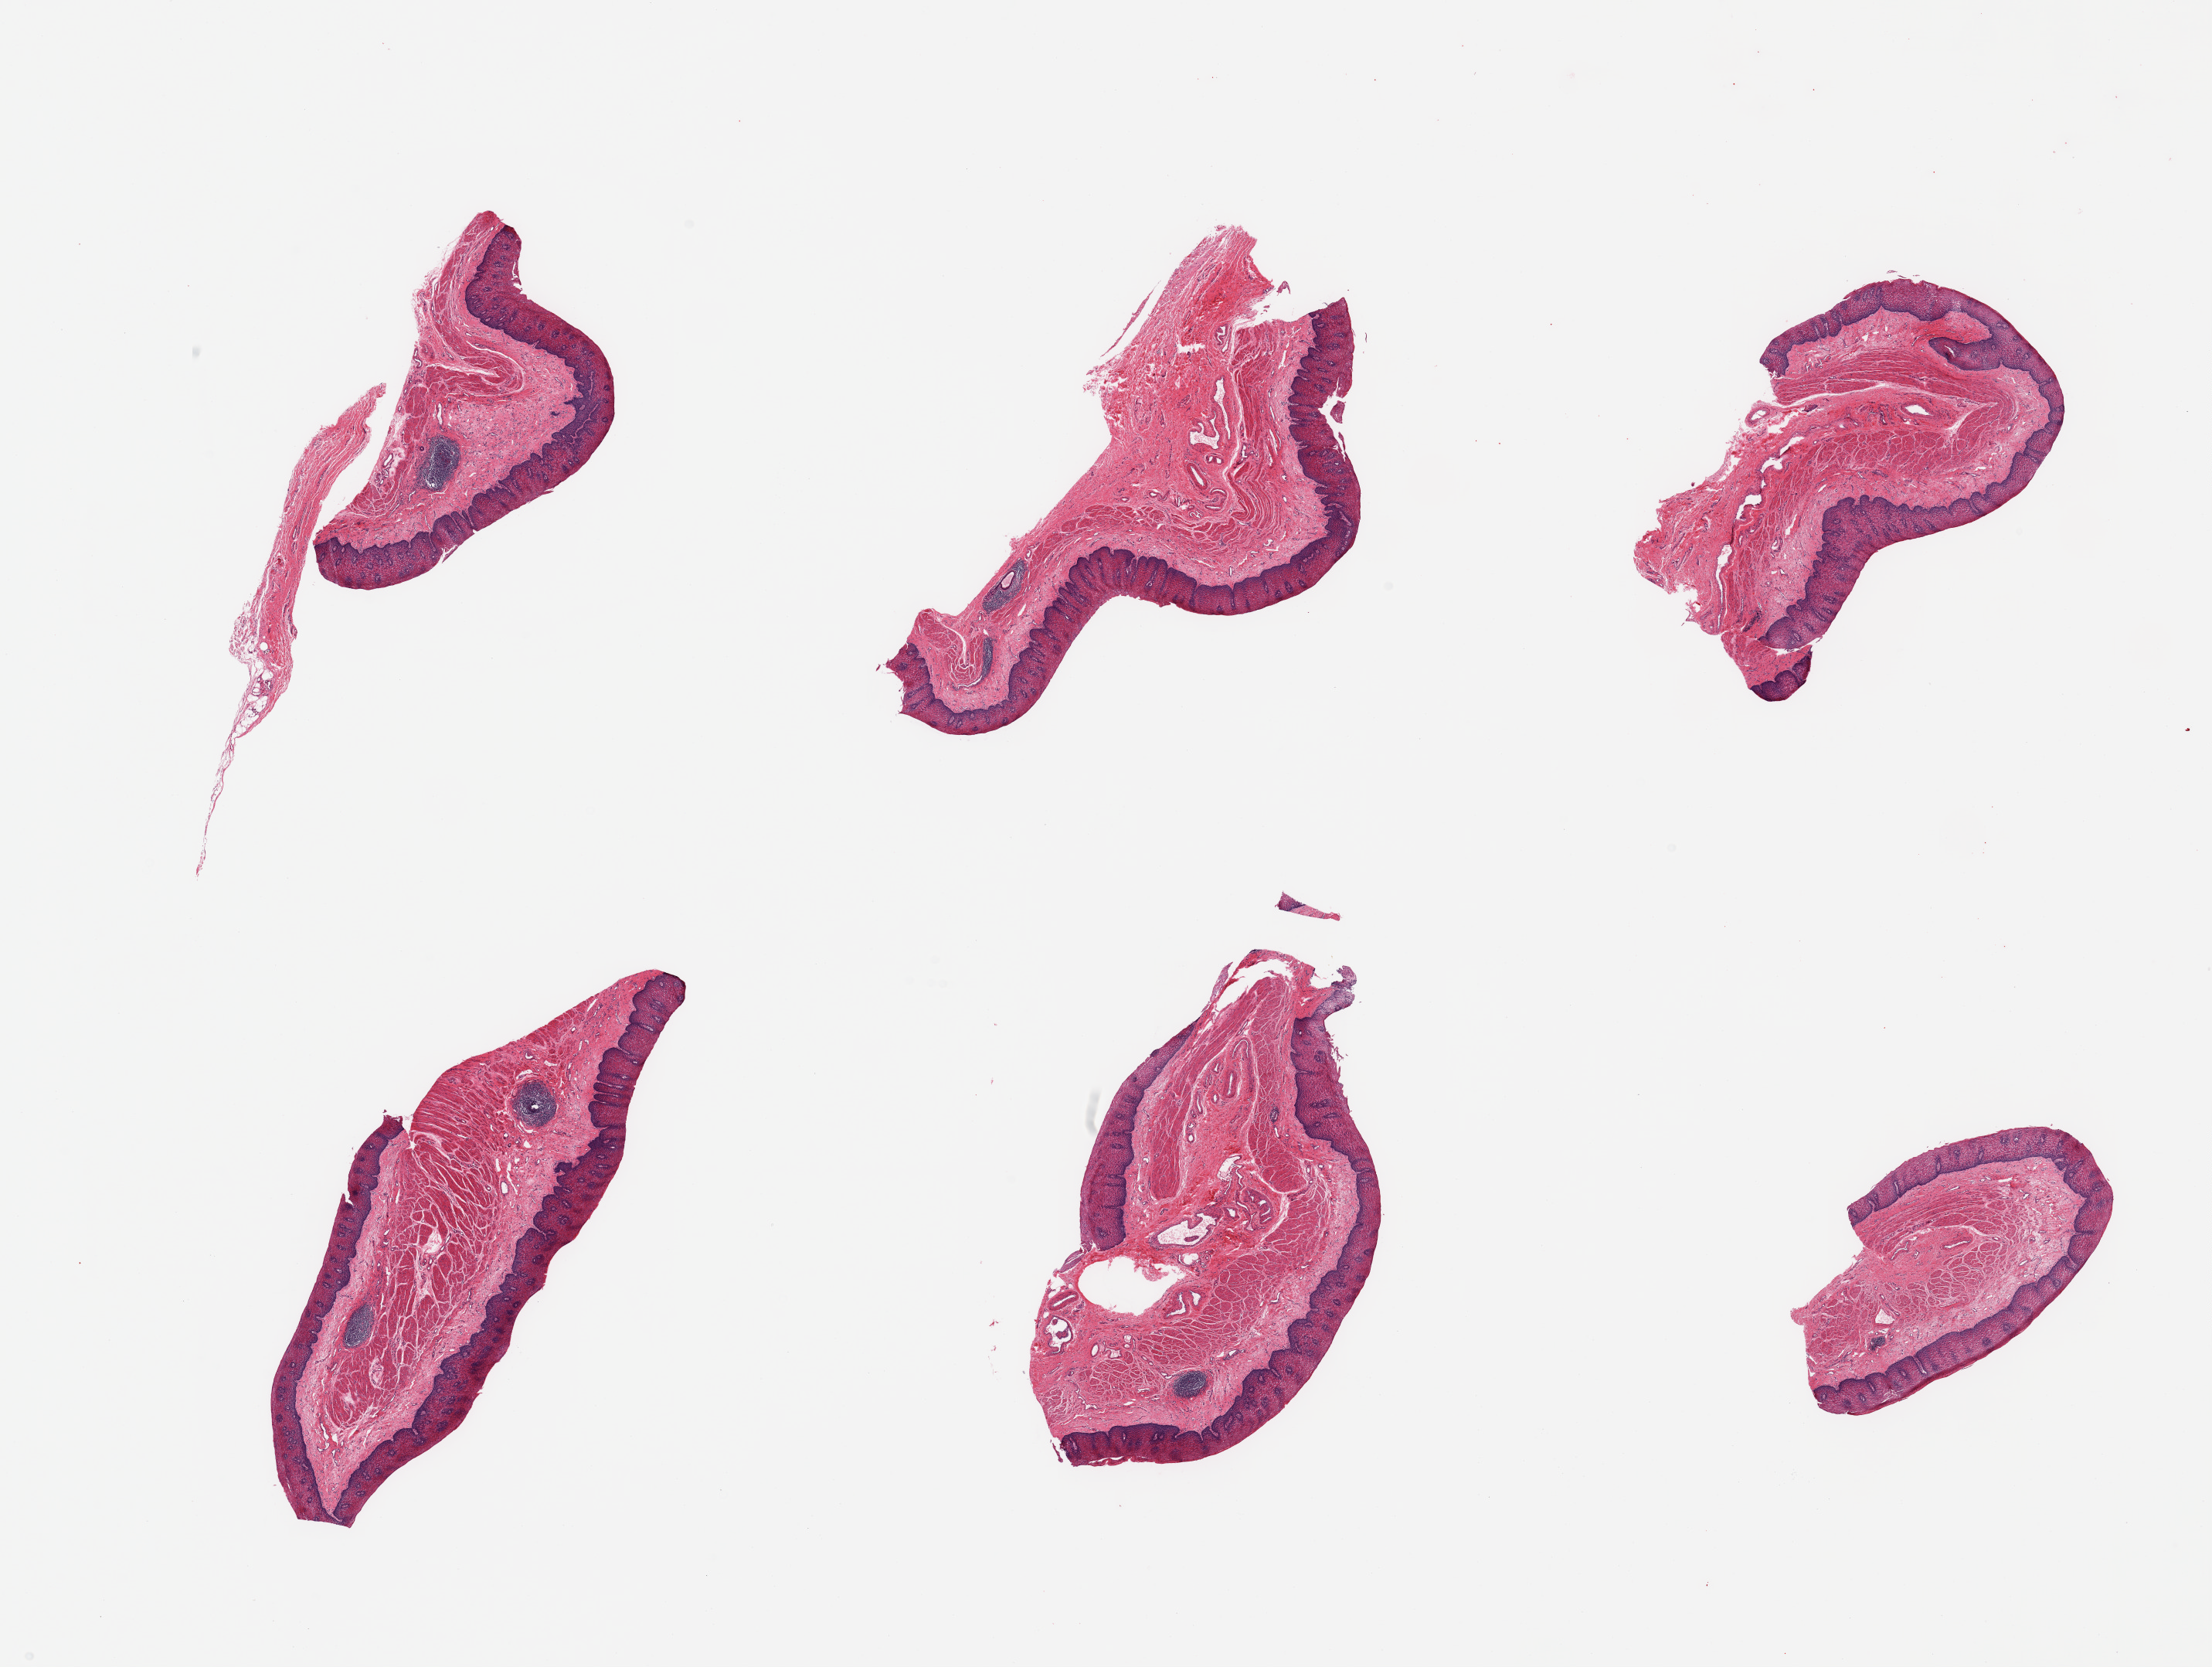
Digitized hematoxylin and eosin (H&E)-stained section — a low-resolution overview of the entire scanned area, about 22.6 x 17.1 mm, PAXgene-fixed, paraffin-embedded tissue, sampled site (target tissue): esophageal mucous membrane, donor tissue sample. Donor: male.
Pathologist's review note for this sample: 6 pieces.